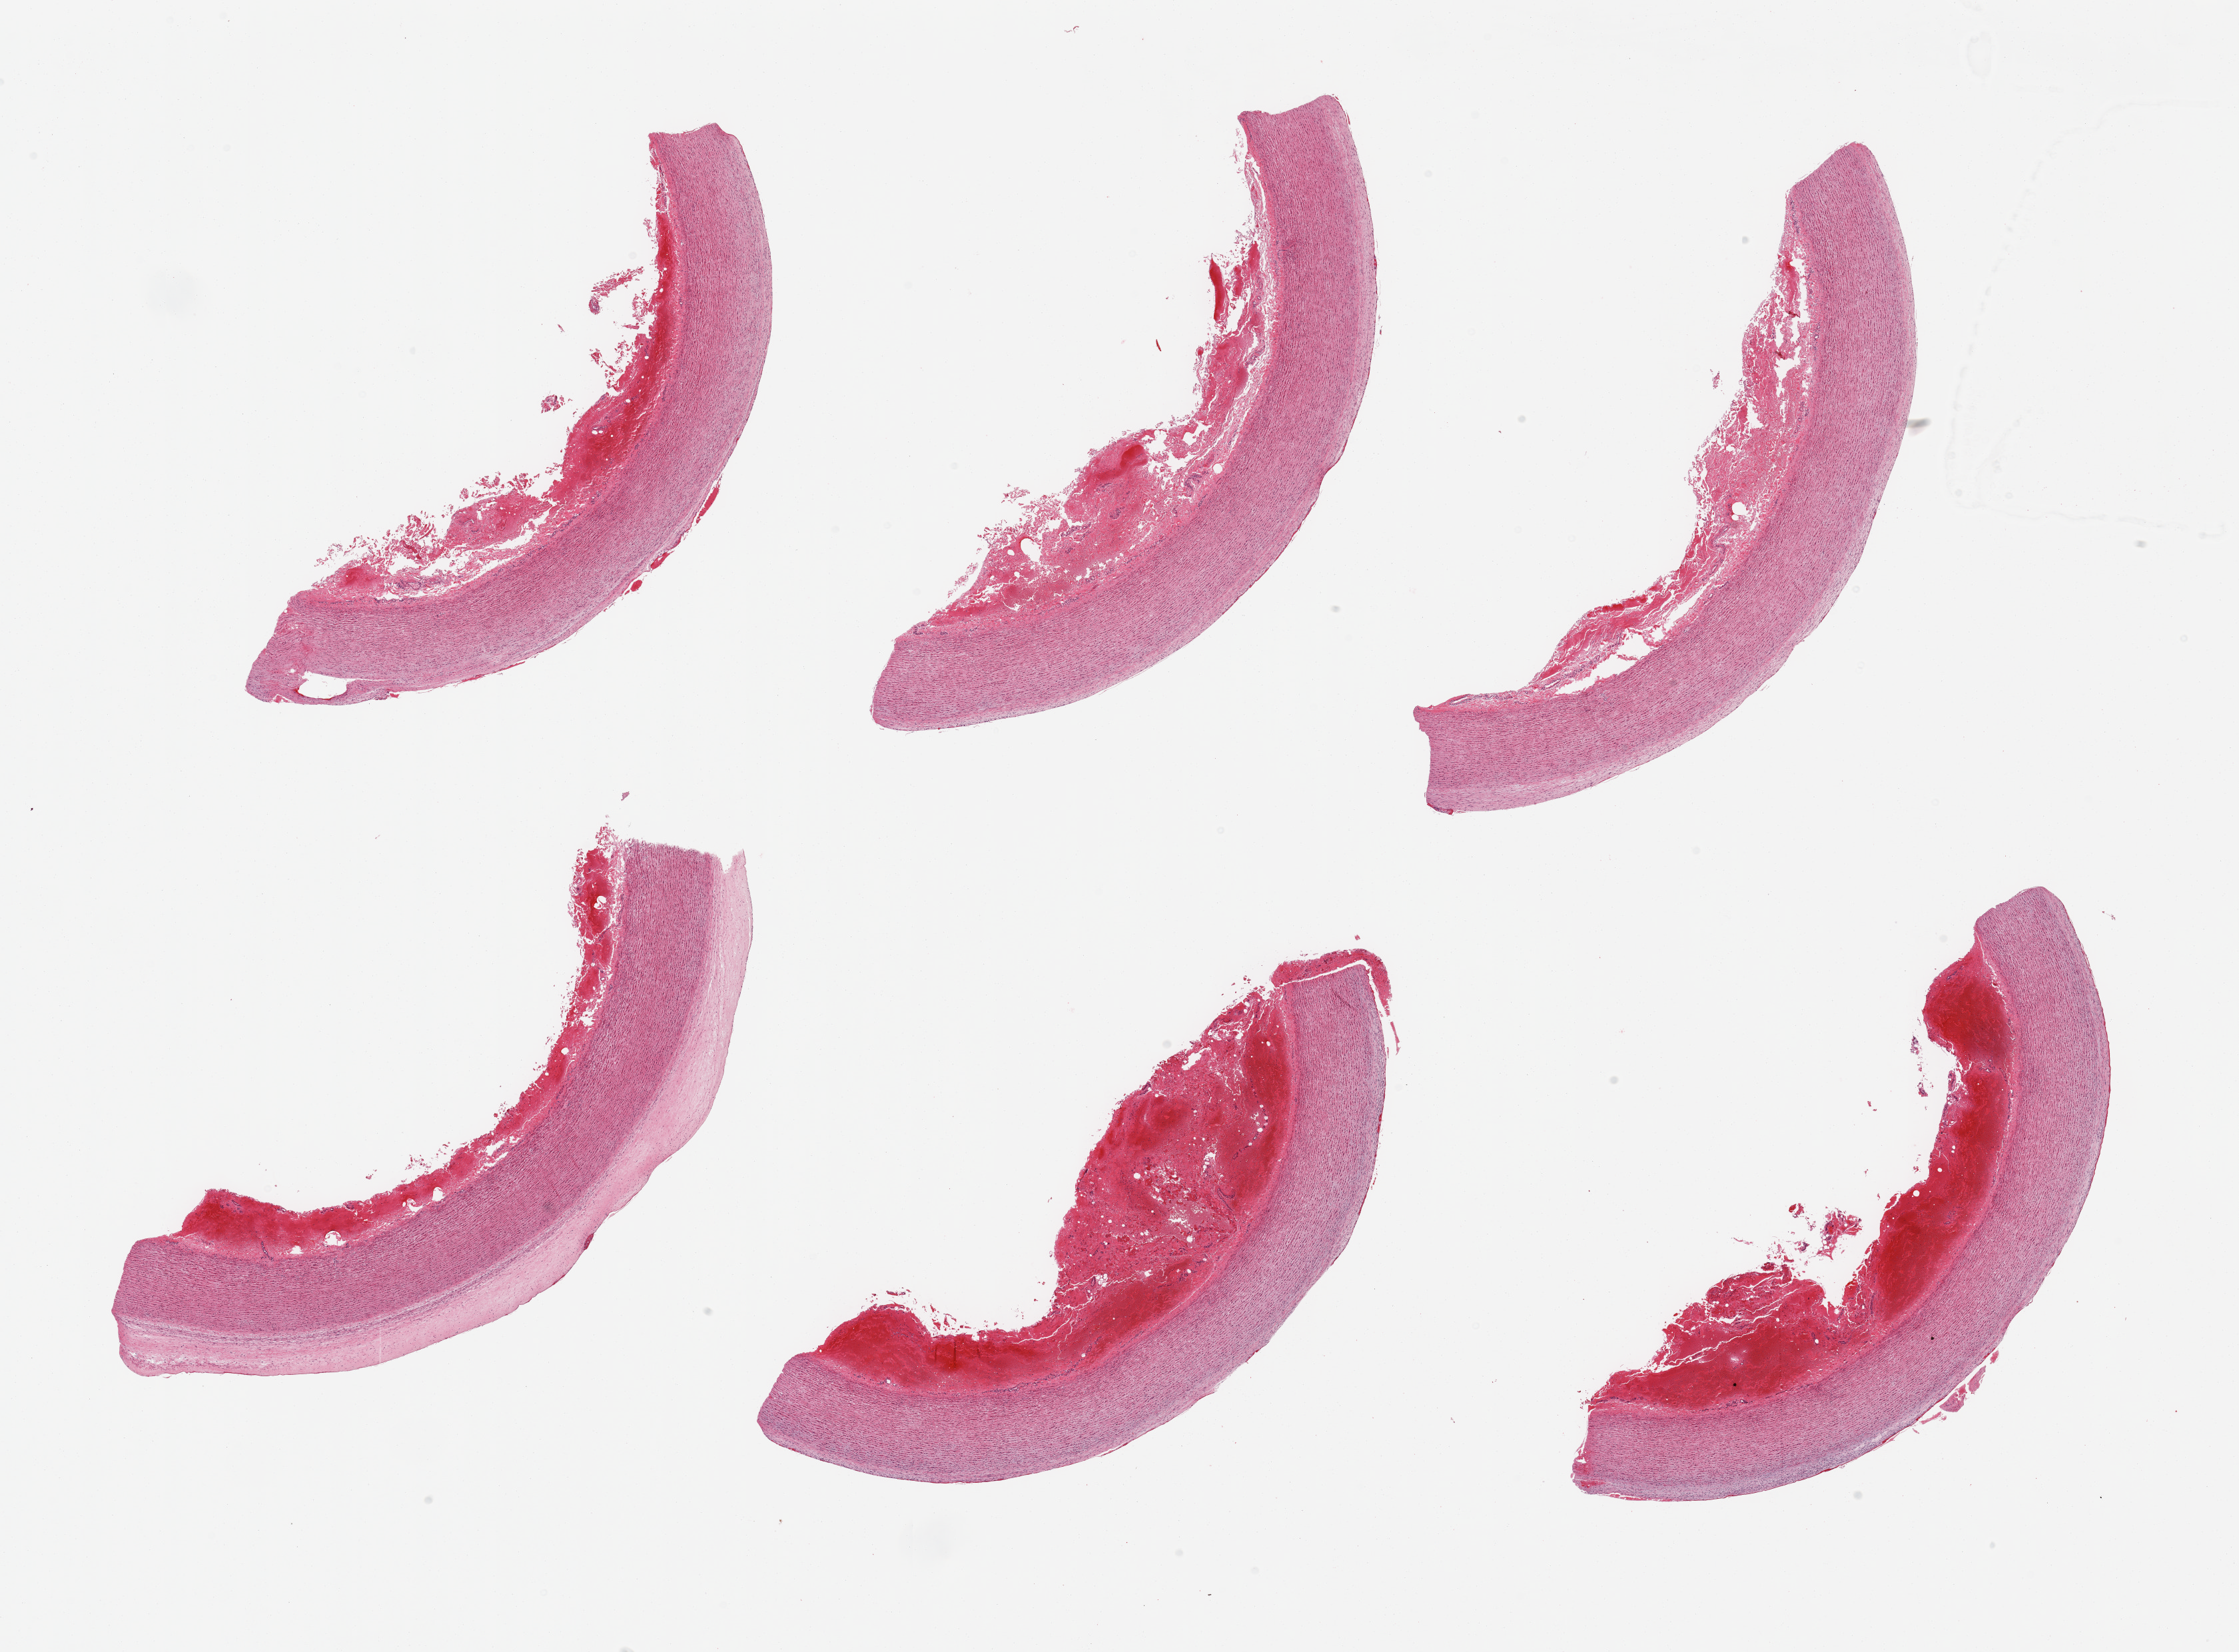
Digitized haematoxylin and eosin-stained section, brightfield — a low-resolution overview of the entire scanned area, about 26.6 x 19.6 mm (slide scanned at 20x). PAXgene-fixed, paraffin-embedded tissue. Target tissue: aorta. Donor tissue sample.
Pathologist's review note for this sample: 6 pieces, atherosis up to ~0.5mm.